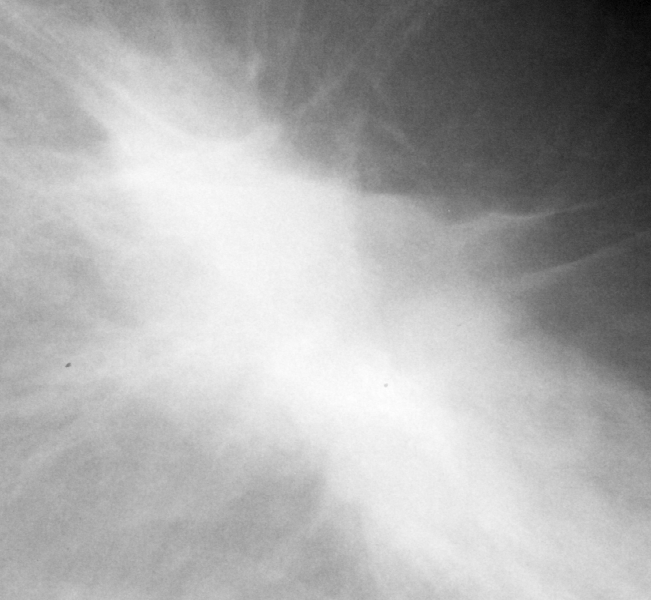
Region of interest cut from a scanned film mammogram (one marked finding), left breast, MLO view.
Mass, shape irregular / architectural distortion, margins spiculated; BI-RADS assessment category 5; pathology result (as recorded, not read from the image): malignant.